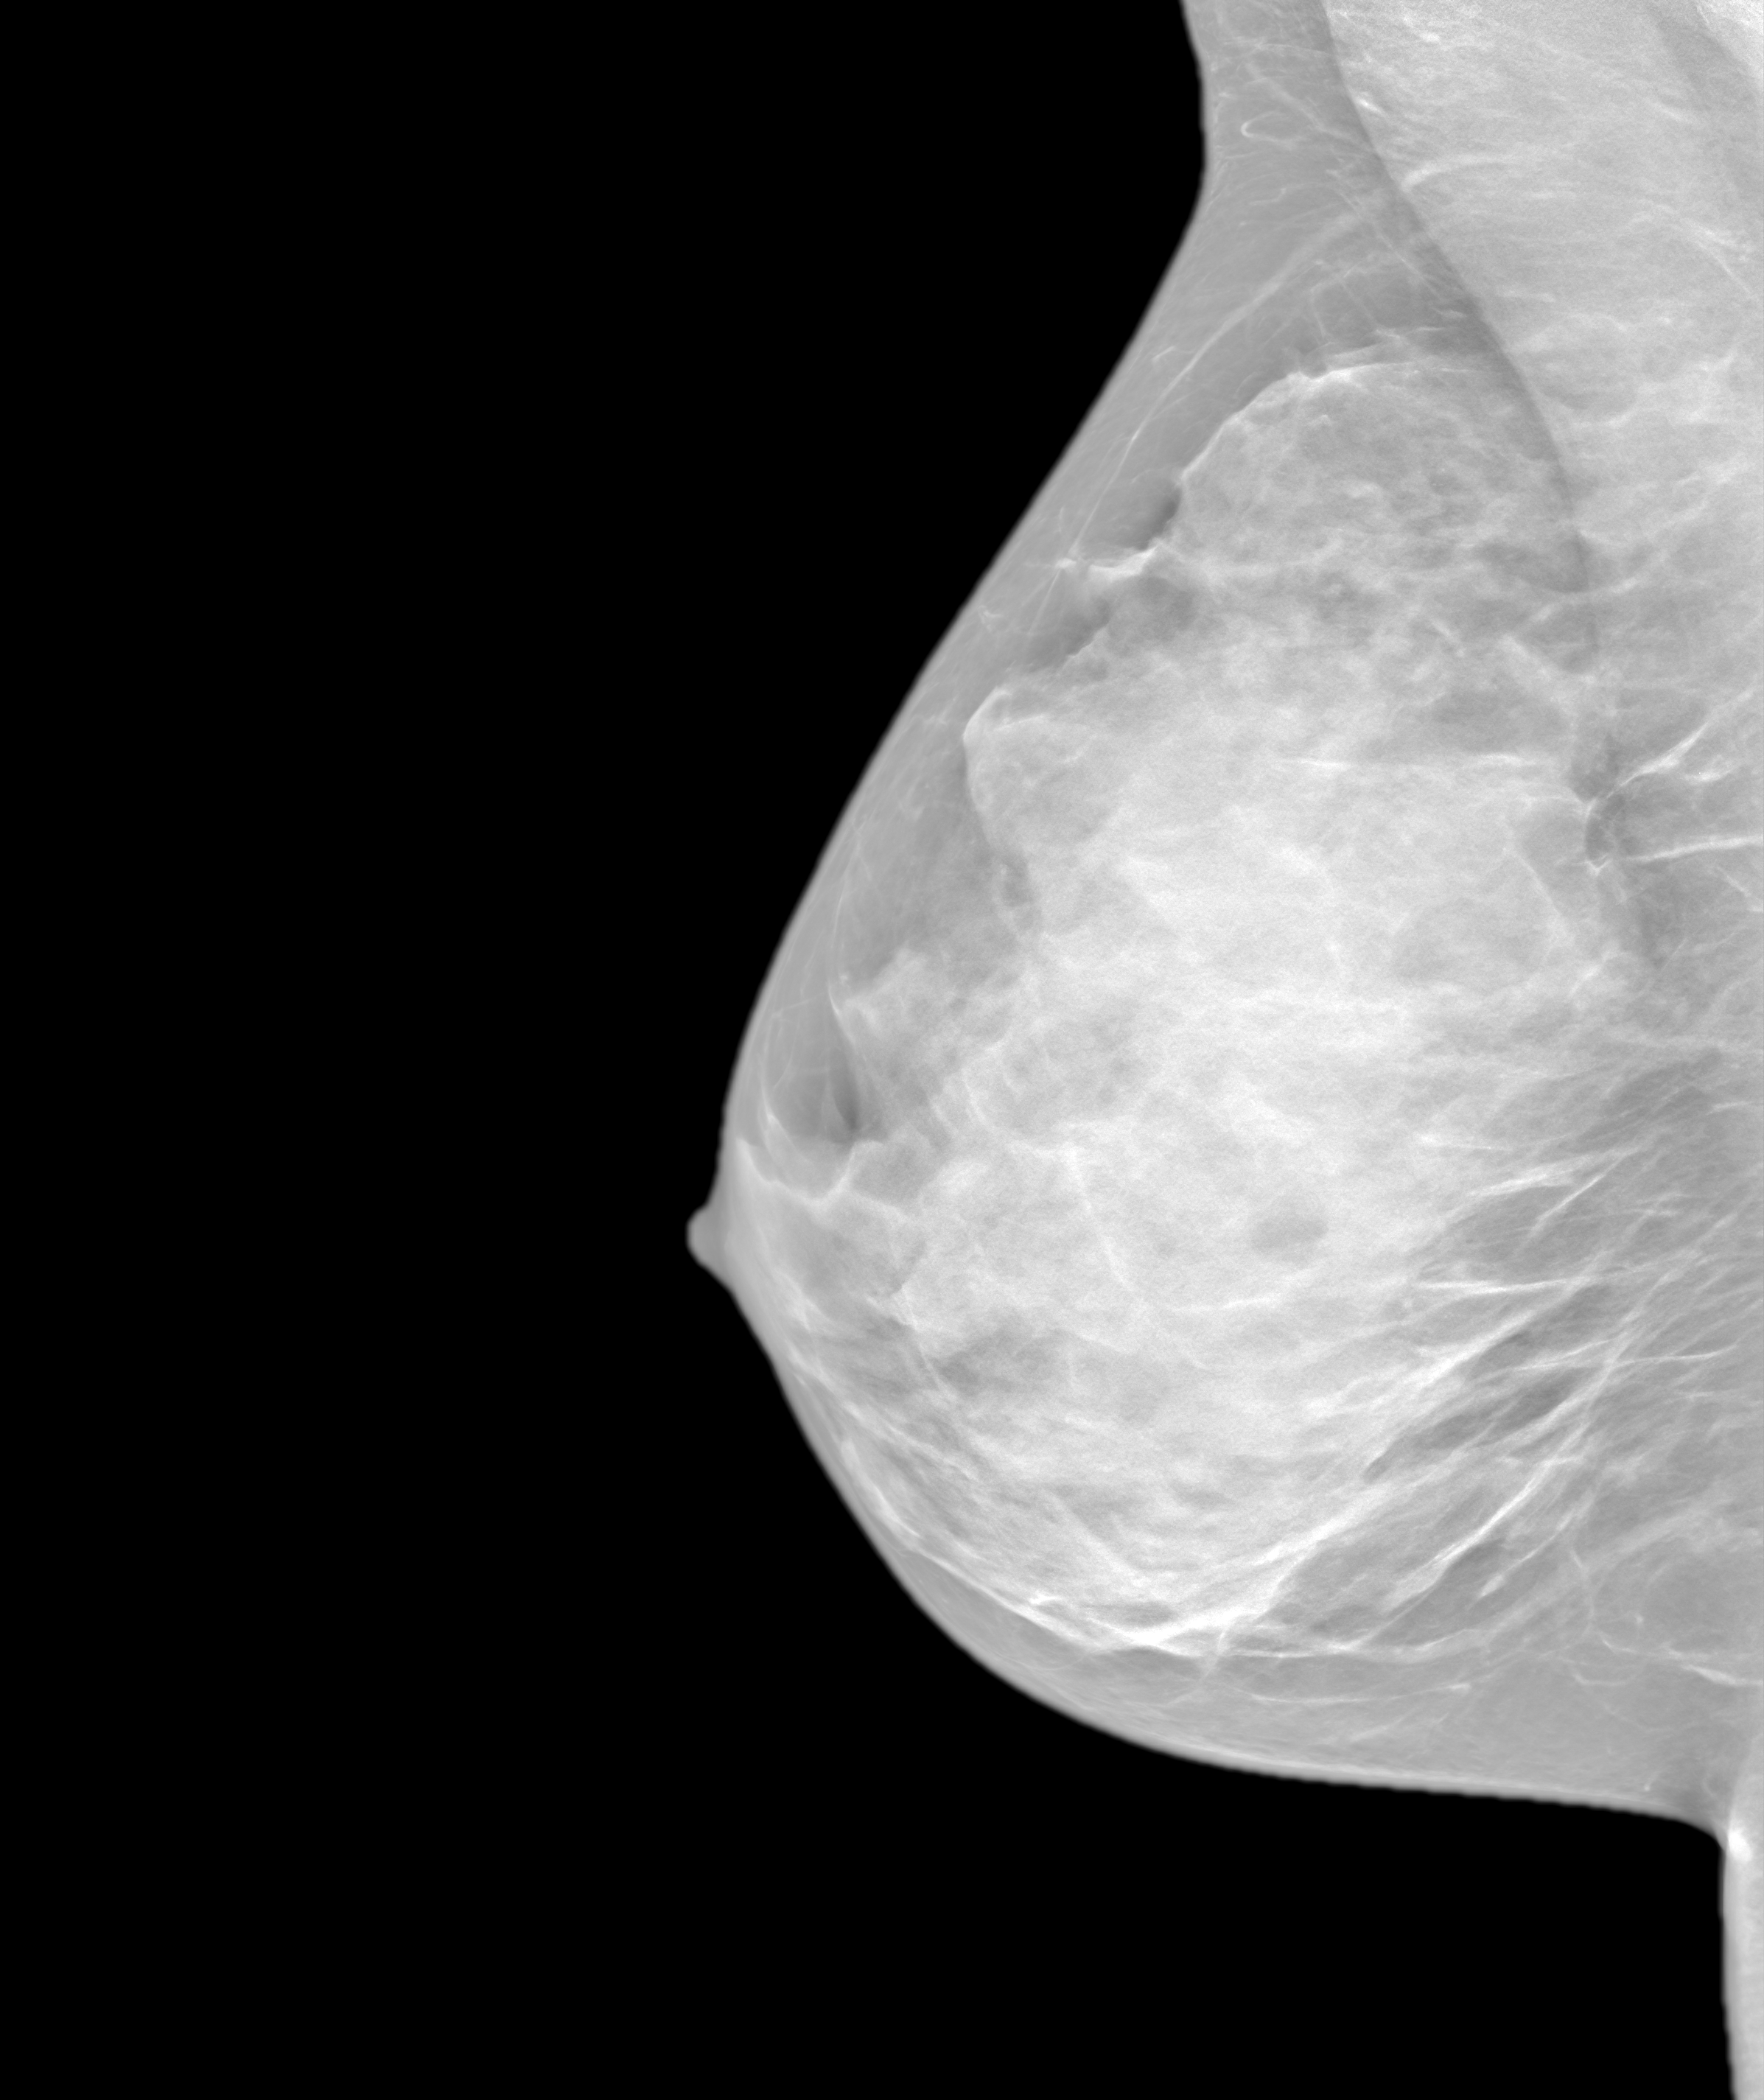
Annual screening mammography examination; system: SenoIris_1SP1.1(421). Patient aged 44 years (female).
Image type: synthesized 2-D view from tomosynthesis. Breast: right. Projection: mediolateral oblique (MLO) view.